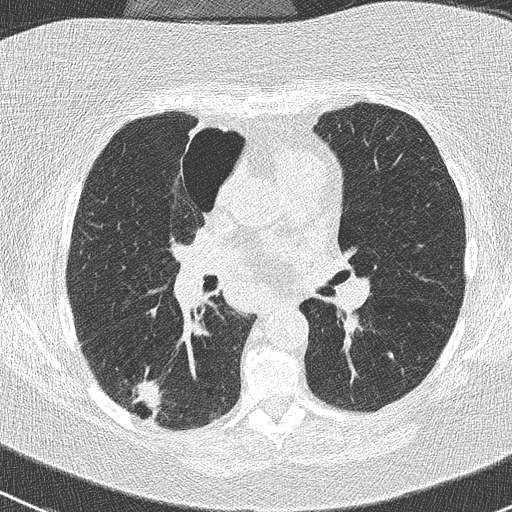
Low-dose screening chest CT, one axial slice. Position 143 of 261 along the scan axis. Lung window (W 1500 / L -600 HU). 2 mm slice thickness. 512 × 512 image matrix, field of view 310 × 310 mm.
Outlined on this slice (outlined manually by an expert reader):
- lesion 1 (tumor, lower lobe of right lung): bounding box [x1, y1, x2, y2] px = [133, 380, 163, 412]